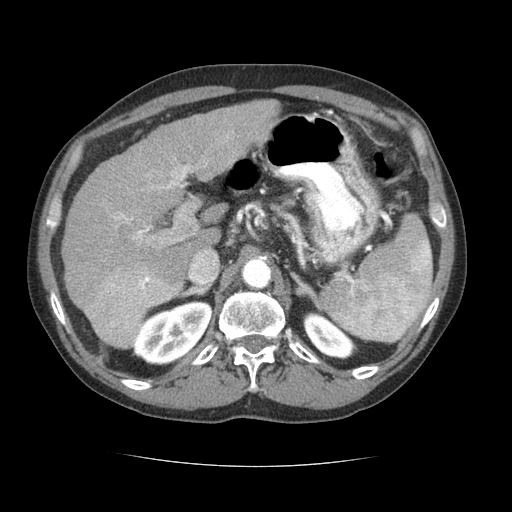
Contrast-enhanced abdominal CT (liver protocol), one axial slice; position 45 of 69 along the scan axis; 120 kVp; soft-tissue window (W 400 / L 40 HU); 2.5 mm slice thickness; 512 × 512 image matrix. Case-level facts recorded for this patient, not image findings: diagnosis: hepatocellular carcinoma (patient treated with transarterial chemoembolisation; whether this scan precedes or follows treatment is not stated here); TNM stage (as recorded): Stage-II; Child-Pugh class: B.
Annotated regions visible in this slice (semi-automatically segmented with operator editing):
- liver parenchyma outside the tumour (the mass and vessels are separate outlines, so this box may not span the whole liver): bounding box [x1, y1, x2, y2] px = [62, 100, 280, 348]
- mass: [83, 260, 180, 347]
- liver vessels: [113, 134, 228, 285]